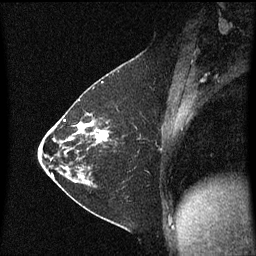
Breast MRI (dynamic contrast-enhanced), one sagittal slice. Slice 29 of 60 in the series (ordered by position). Dynamic contrast-enhanced series, image 2 of 3 at this slice position (ordered by acquisition). 1.5 T. TE 4.2 ms, TR 8.4 ms. 256 × 256 image matrix, field of view 200 × 200 mm. Patient: female, 36 years. From the clinical record (not read from this slice): setting: breast cancer imaged before/during neoadjuvant chemotherapy; receptor status: HR-positive, HER2-negative.
Structures marked on this image (semi-automatically segmented with operator editing):
- analysis volume of interest (the breast-tissue region the enhancement analysis was run in; not a lesion): bounding box (x1, y1, x2, y2) in pixels: (72, 116, 119, 187)
- tumour enhancement mask (voxels above the 70 % enhancement threshold inside the analysis volume of interest): (72, 122, 109, 181)